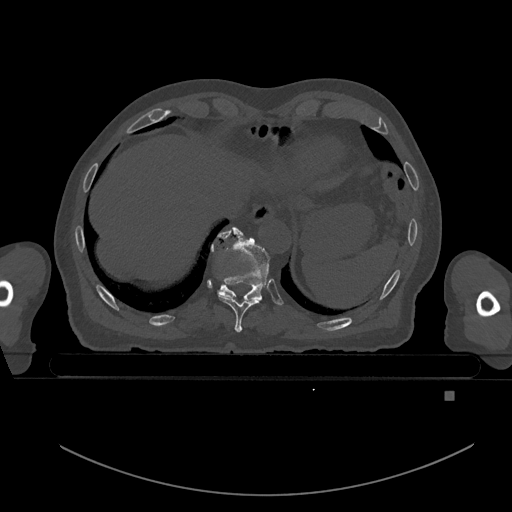
CT including the spine, one axial slice; slice 119 of 969 in the series (ordered by position); bone window (W 1800 / L 400 HU); 0.5 mm slice thickness; 512 × 512 image matrix, field of view 456 × 456 mm. Patient: male, 82 years. From the clinical record (not read from this slice): primary cancer: prostate; vertebrae with lytic lesions (as recorded): T11, T9, T8, T2.
Outlined on this slice (semi-automatically segmented with operator editing):
- T10 vertebra: bounding box [x1, y1, x2, y2] px = [211, 227, 270, 300]
- T9 vertebra: [218, 230, 262, 333]